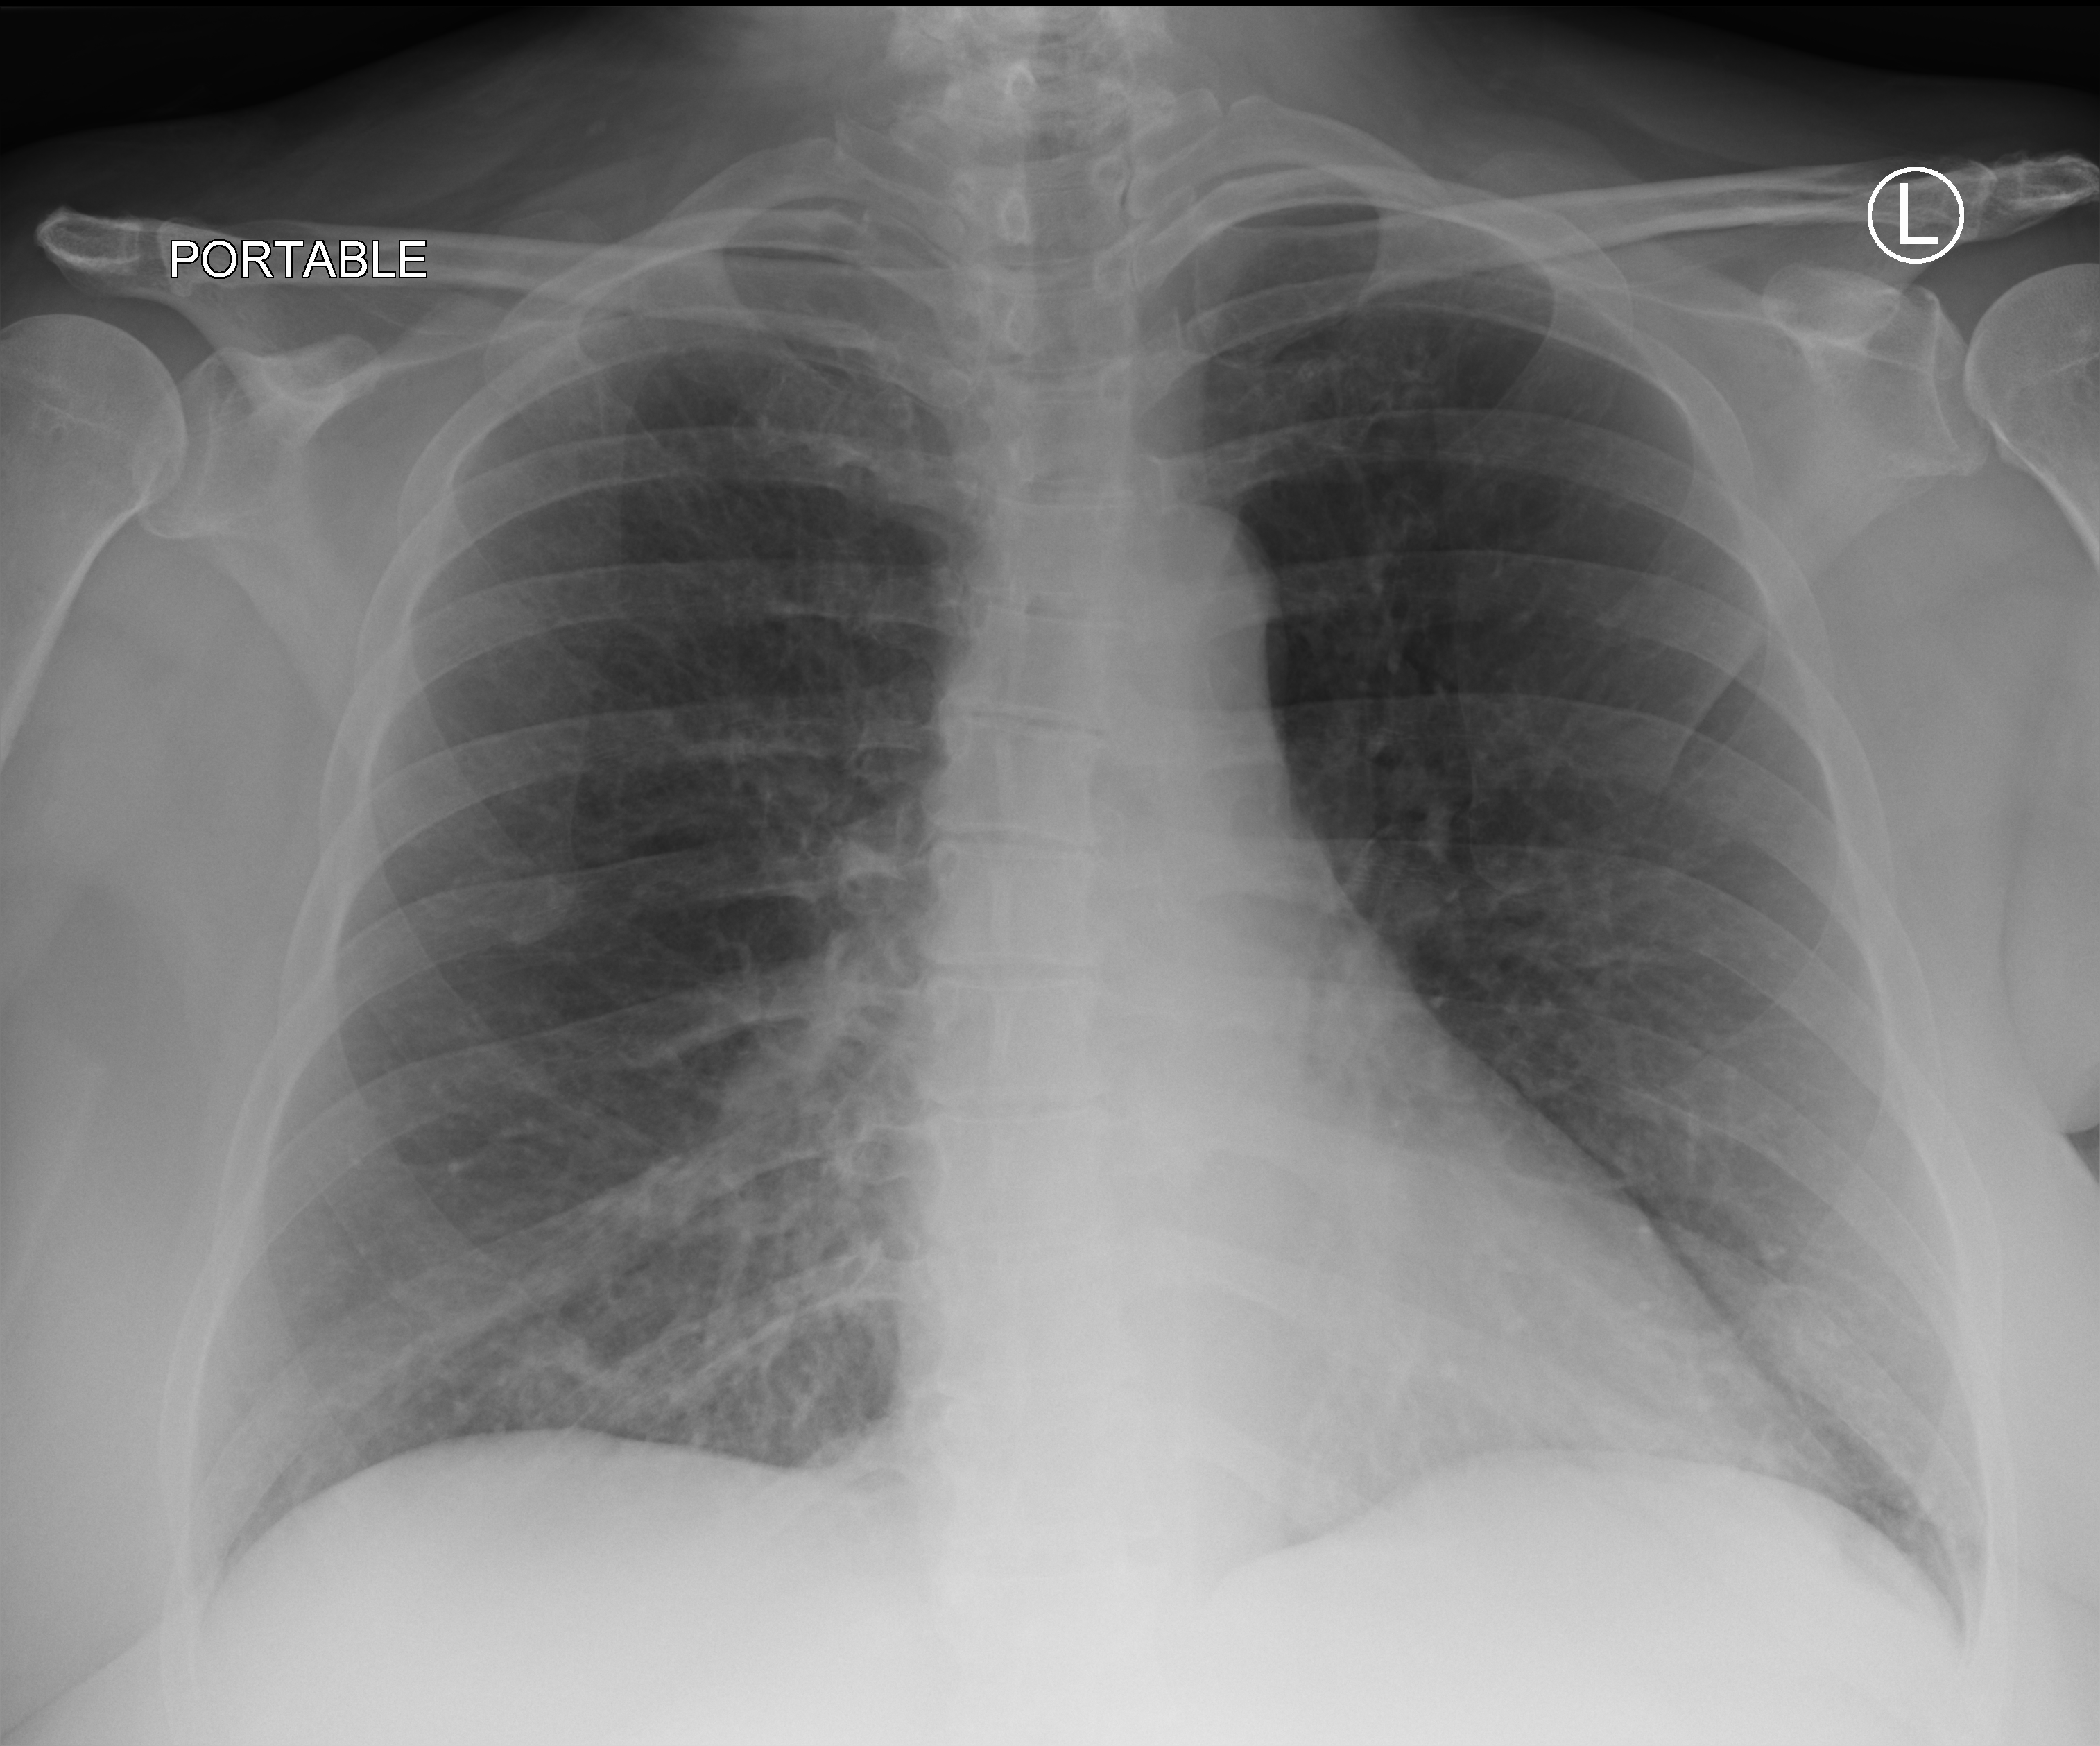
Bedside chest radiograph (computed radiography); anteroposterior (AP) projection. Patient hospitalised with COVID-19; female, aged 18–59 years.
Admission-level facts for this patient (not findings on this image; timing relative to this image not recorded):
- admitted to intensive care during this hospital stay: no
- smoking status (admission record): current